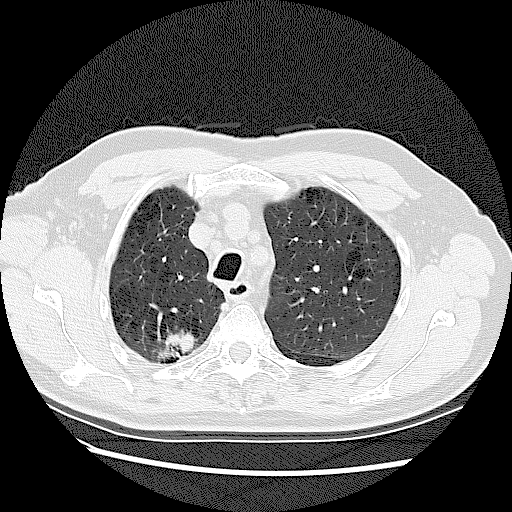
Chest CT (low-dose screening protocol), one axial image; baseline annual screen; lung window (W 1500 / L -600 HU); 2.5 mm slice thickness; slice 30 of 128 in the series; 512 × 512 image matrix, field of view 360 × 360 mm. Male participant, aged 72 years at enrolment.
• Lesion marked by an expert reader, bounding box <134,307,213,375> (left, top, right, bottom; pixels).
• The screening reader recorded 2 non-calcified nodules or masses ≥4 mm on this exam (right upper lobe, right upper lobe); which of them this box marks is not recorded.
• Lung cancer was diagnosed 42 days after this screen: adenocarcinoma, NOS, right upper lobe, stage IV (AJCC 6th edition), 45 mm at pathology.